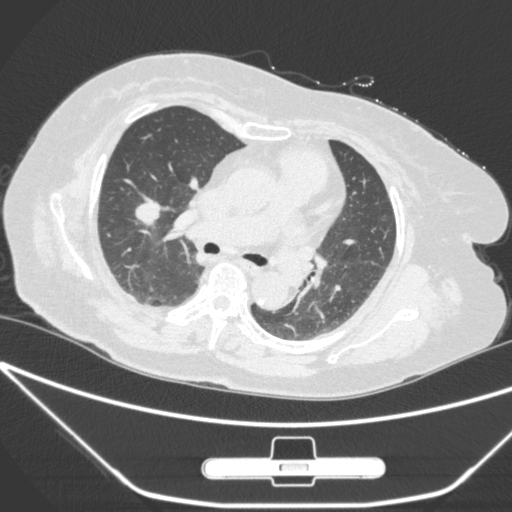
Chest CT, one axial slice; slice 159 of 245 in the series (ordered by position); 120 kVp; lung window (W 1500 / L -600 HU); 1 mm slice thickness; 512 × 512 image matrix, field of view 365 × 365 mm. Patient: female, 65 years. From the clinical record (not read from this slice): clinical TNM (as recorded): T1c N0 M0; histopathological grade: G3.
Annotated regions visible in this slice (bounding box drawn by a radiologist):
- lung tumour (recorded histology: adenocarcinoma): bounding box <133,194,163,236> (left, top, right, bottom; pixels)